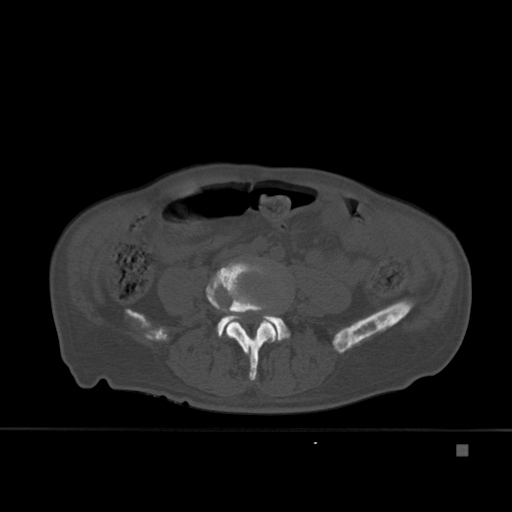
CT including the spine, one axial slice. Position 116 of 451 along the scan axis. Bone window (W 1800 / L 400 HU). 1.5 mm slice thickness. 512 × 512 image matrix, field of view 378 × 378 mm. Male patient, age 75 years. From the clinical record (not read from this slice): primary cancer: prostate.
Annotated regions visible in this slice (semi-automatically segmented with operator editing):
- L4 vertebra: bounding box (x1, y1, x2, y2) in pixels: (206, 260, 279, 381)
- L5 vertebra: (217, 315, 290, 342)
- T7 vertebra: (216, 313, 279, 333)